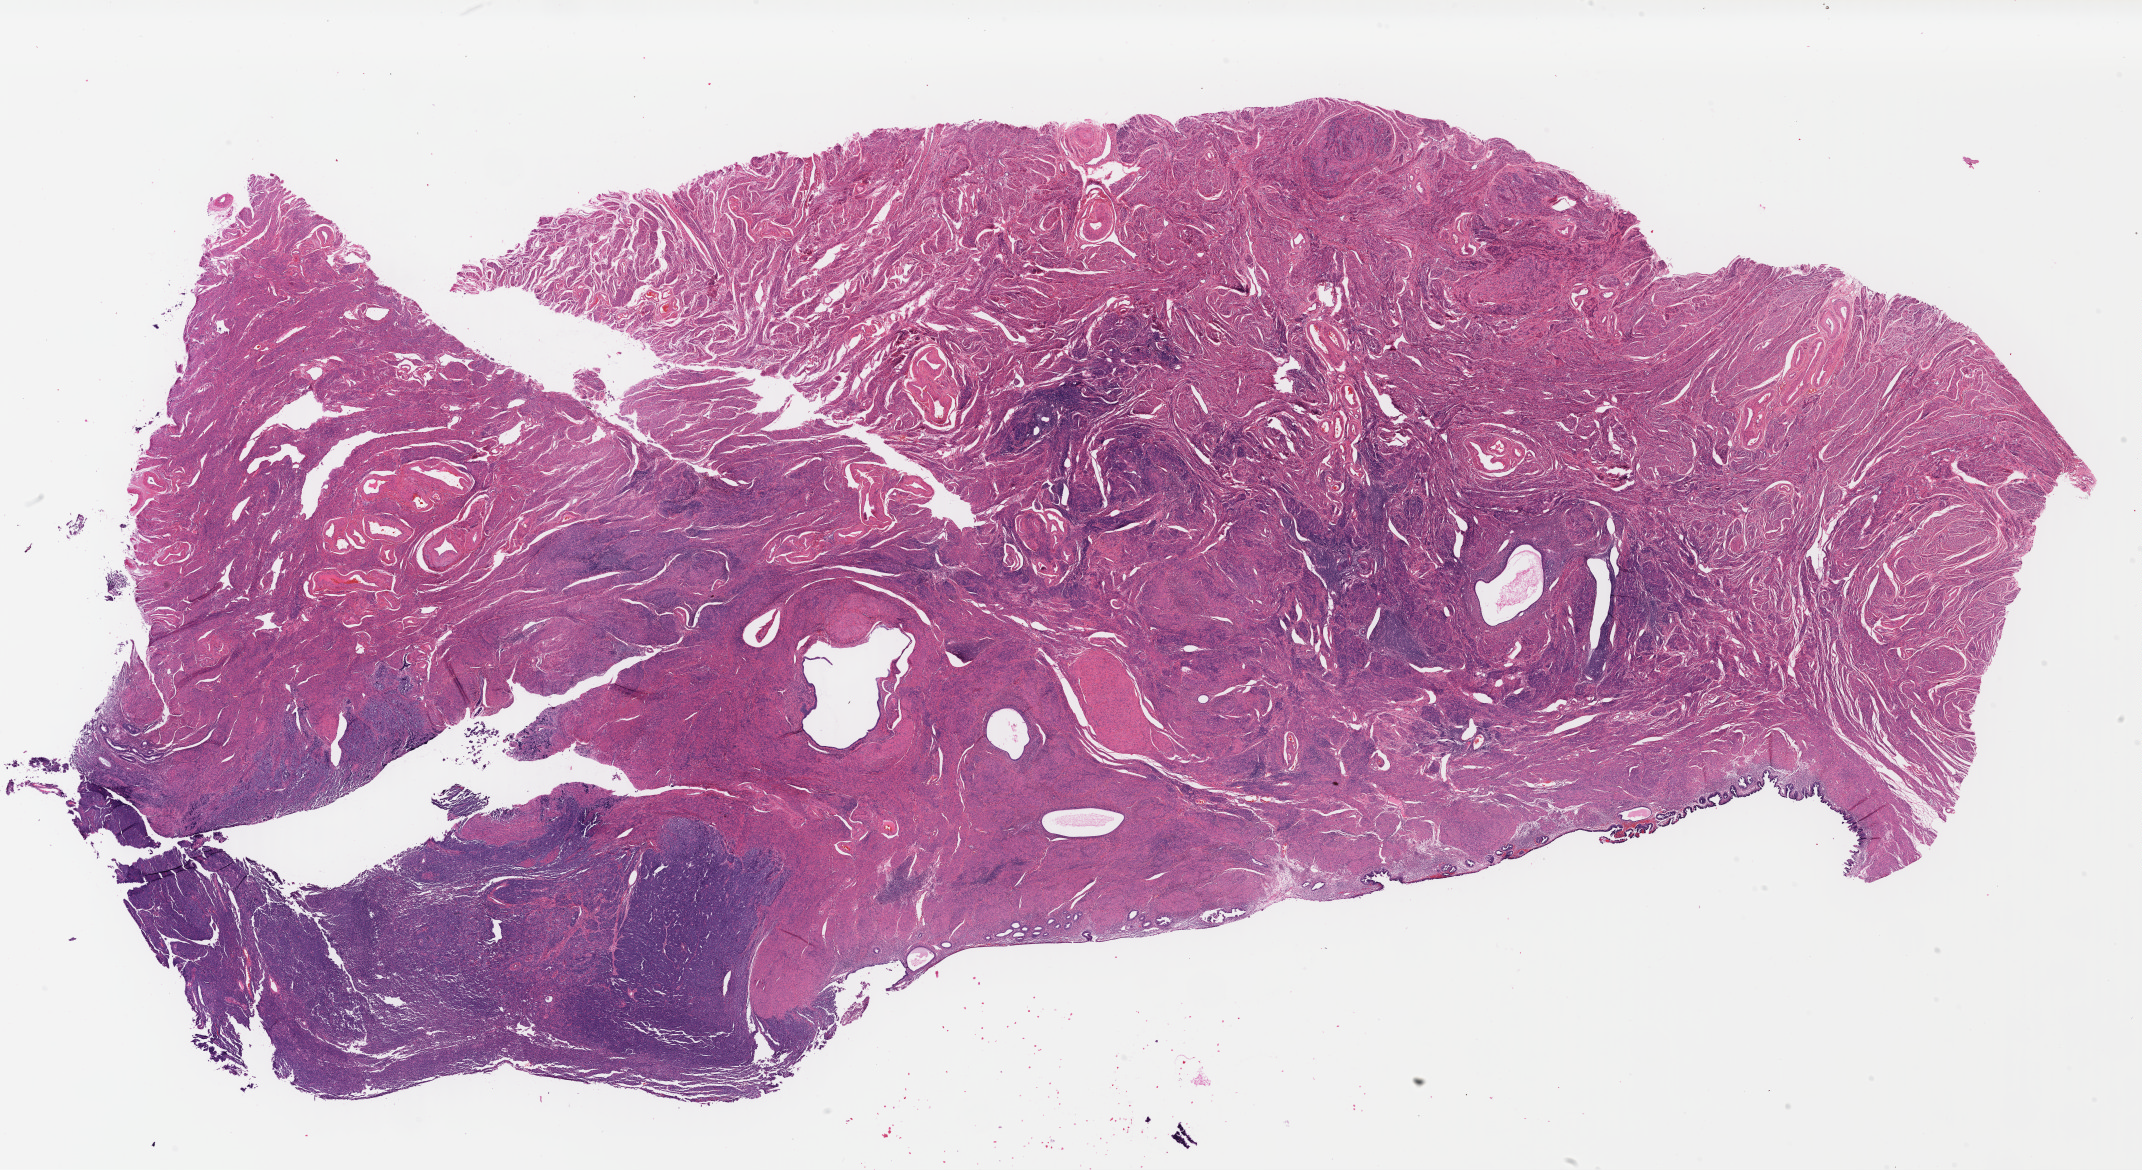
Digitized H&E tissue section (whole slide), shown as a low-resolution overview of the whole scanned area (about 33.7 x 18.4 mm, acquisition: 40x scan); FFPE section; uterus, primary tumour sample. Female, age 73 years at initial diagnosis.
Diagnosis: Endometrioid adenocarcinoma, NOS (endometrium).